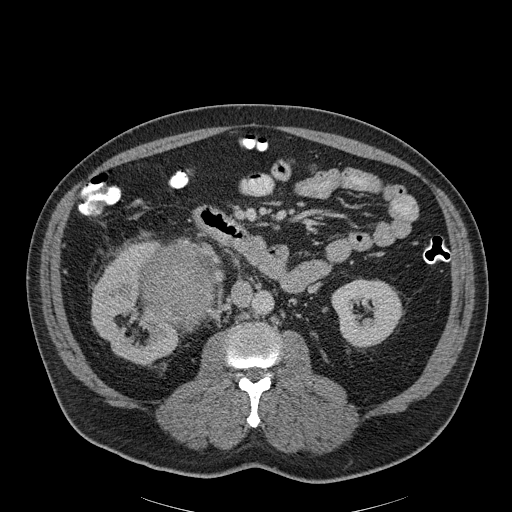
Contrast-enhanced abdominal CT, one axial slice; 120 kVp; soft-tissue window (W 400 / L 40 HU); 3 mm slice thickness; 512 × 512 image matrix, field of view 464 × 464 mm. Patient: male, 56 years. Case-level facts recorded for this patient, not image findings: diagnosis: adrenocortical carcinoma; tumour side: right adrenal; tumour size at pathology: 18 cm; Ki-67 index: 2 %; stage (as recorded): 3.
Structures marked on this image (semi-automatic segmentation, software-assisted and operator-edited):
- mass: box from (x=142, y=243) to (x=213, y=329) px